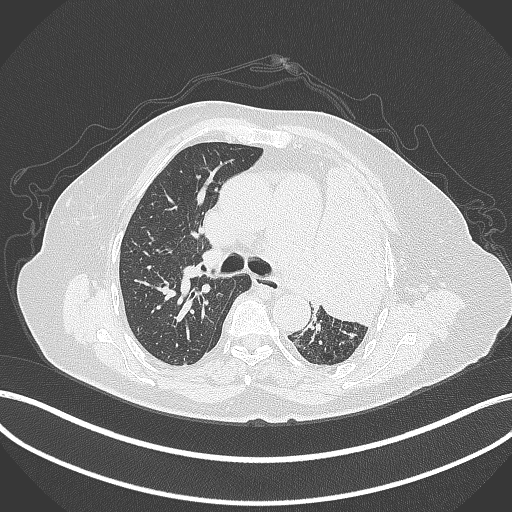
Chest CT, one axial slice; reconstruction kernel B70f; 120 kVp; lung window (W 1500 / L -600 HU); 1 mm slice thickness; 512 × 512 image matrix. Female patient, age 75 years. From the clinical record (not read from this slice): clinical TNM (as recorded): T3 N3 M1.
Structures marked on this image (bounding box drawn by a radiologist):
- lung tumour (recorded histology: adenocarcinoma): bounding box (x1, y1, x2, y2) in pixels: (312, 156, 397, 330)